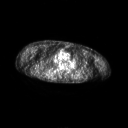
FDG PET of an extremity soft-tissue mass (from a PET/CT study), one axial slice; position 177 of 267 along the scan axis; 3.27 mm slice thickness; 128 × 128 image matrix. Male patient, age 61 years. Case-level facts recorded for this patient, not image findings: histological type: pleiomorphic spindle cell undifferentiated; grade: high; site of the primary tumour: right parascapusular.
Annotated regions visible in this slice (expert contour drawn on MRI and transferred to this co-registered scan by the dataset authors):
- gross tumour volume including surrounding oedema: bounding box (x1, y1, x2, y2) in pixels: (39, 71, 59, 78)